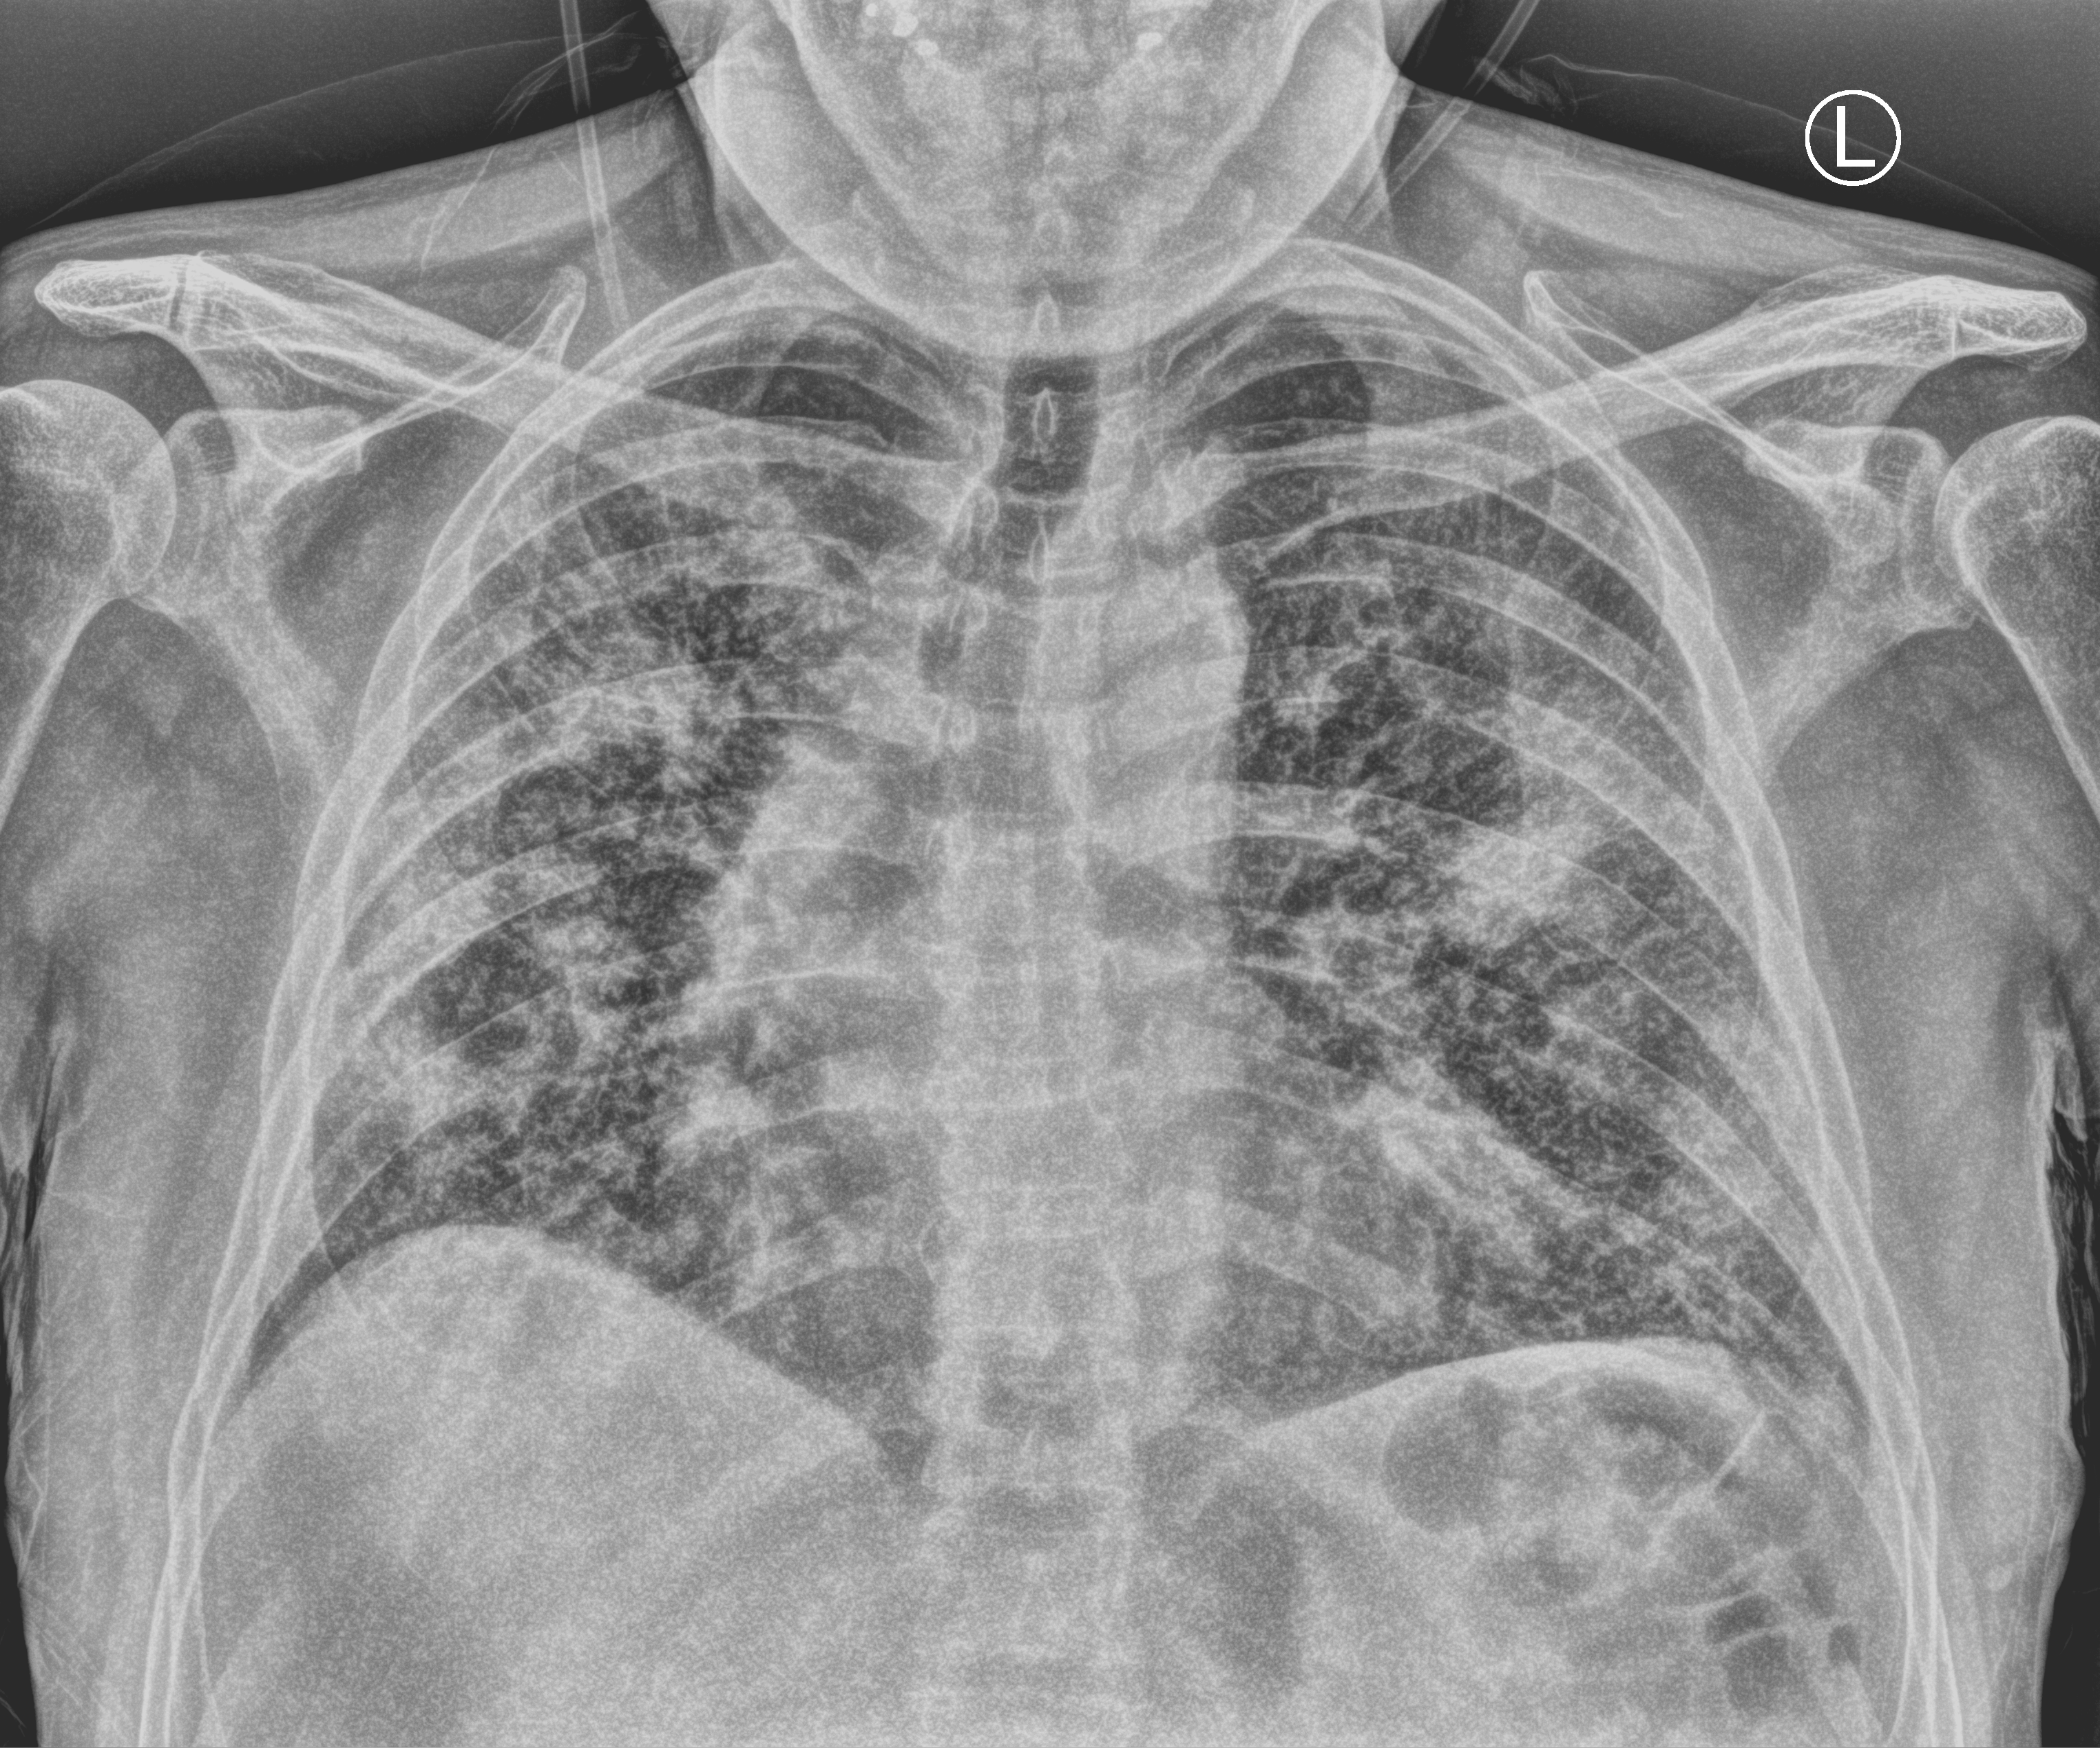
Bedside chest radiograph (computed radiography); anteroposterior (AP) projection. Patient hospitalised with COVID-19; male, aged 60–74 years.
Hospital-stay facts (about this admission, not read from this image; timing relative to this image not recorded):
- mechanically ventilated during this hospital stay: yes
- admitted to intensive care during this hospital stay: yes